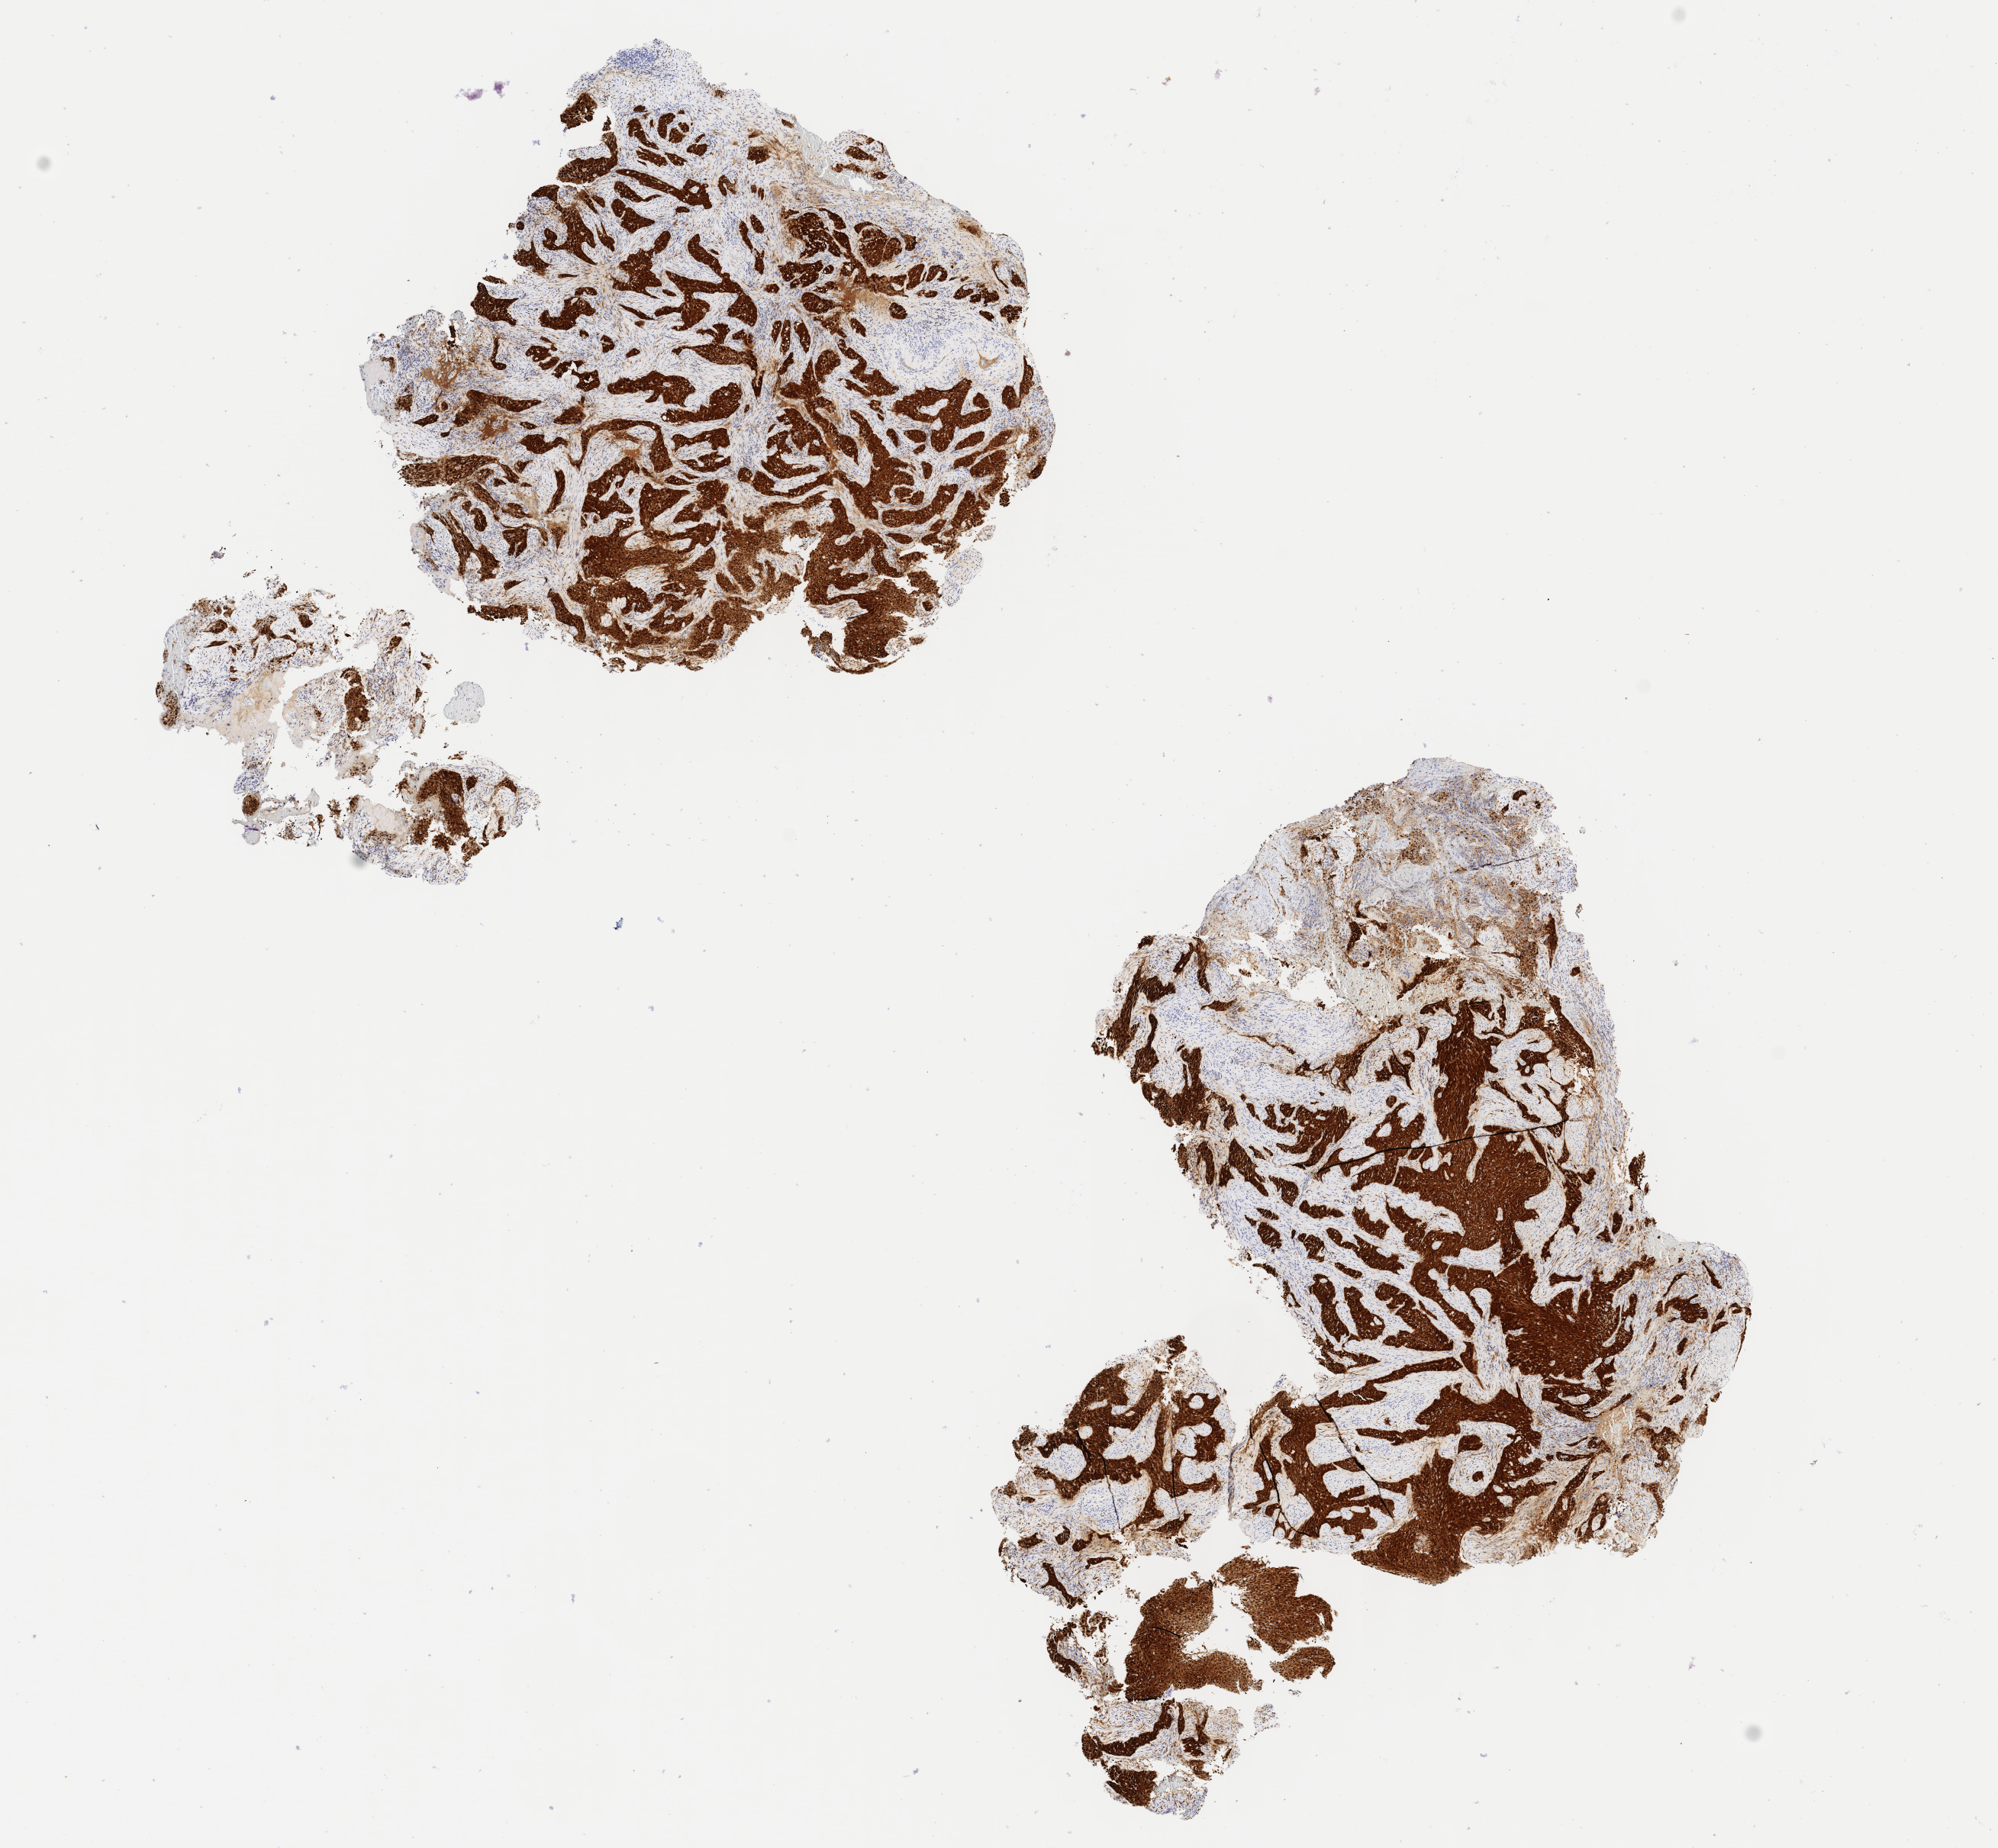
Immunohistochemistry (IHC) whole-slide image stained for p16 (p16INK4a) — low-resolution overview of the scanned area, about 10.4 x 9.6 mm, specimen: tumor tissue, anatomic site: cervix. Patient: female, aged 66.
Histologic diagnosis: Squamous cell carcinoma, large cell, nonkeratinizing, NOS.